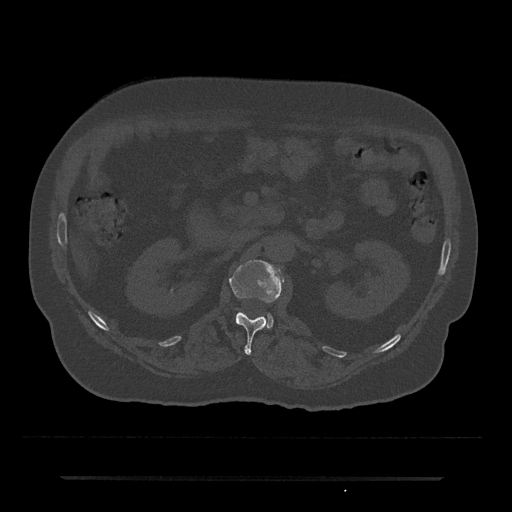
CT including the spine, one axial slice; slice 56 of 797 in the series (ordered by position); reconstruction kernel Br40s/3; bone window (W 1800 / L 400 HU); 512 × 512 image matrix, field of view 437 × 437 mm. Male patient, age 69 years. From the clinical record (not read from this slice): primary cancer: prostate.
Structures marked on this image (semi-automatically segmented with operator editing):
- L1 vertebra: bounding box [x1, y1, x2, y2] px = [229, 260, 284, 354]
- L2 vertebra: [265, 314, 274, 328]